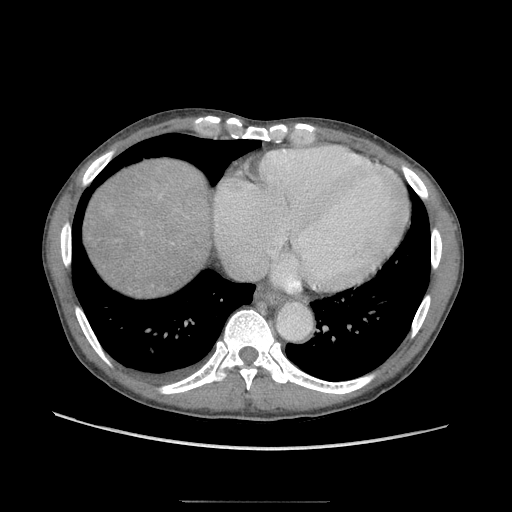
Contrast-enhanced abdominal CT (liver protocol), one axial slice; reconstruction kernel STANDARD; 120 kVp; soft-tissue window (W 400 / L 40 HU); 2.5 mm slice thickness; 512 × 512 image matrix, field of view 380 × 380 mm. Case-level facts recorded for this patient, not image findings: diagnosis: hepatocellular carcinoma (patient treated with transarterial chemoembolisation; whether this scan precedes or follows treatment is not stated here); TNM stage (as recorded): Stage-IIIA; Child-Pugh class: A; tumour differentiation: moderately differentiated; tumour nodularity: multinodular.
Annotated regions visible in this slice (semi-automatically segmented with operator editing):
- abdominal aorta: bounding box <277,303,310,339> (left, top, right, bottom; pixels)
- liver parenchyma outside the tumour (the mass and vessels are separate outlines, so this box may not span the whole liver): <88,162,206,286>